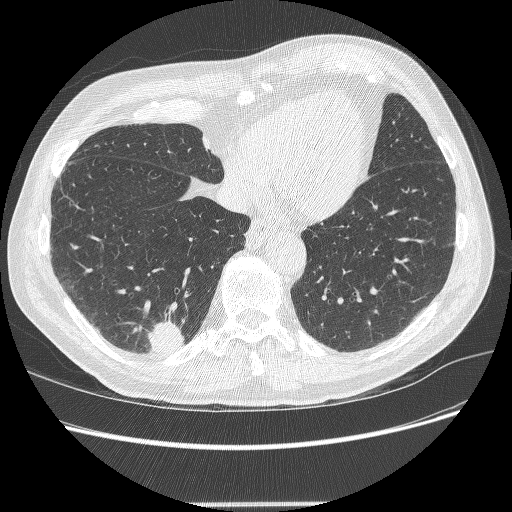
Low-dose screening chest CT, axial slice. Second screening round (one year after baseline). Lung window (W 1500 / L -600 HU). 1.25 mm slice thickness. Lung (sharp) reconstruction kernel (BONE). Slice 67 of 245 in the series. 512 × 512 image matrix. Male, age 71 years at enrolment. Current smoker at enrolment.
Expert reader's lesion annotation, bounding box <137,322,188,361> (left, top, right, bottom; pixels). The screening reader recorded 5 non-calcified nodules or masses ≥4 mm on this exam (right lower lobe, right lower lobe, right upper lobe, right upper lobe, right upper lobe); which of them this box marks is not recorded.